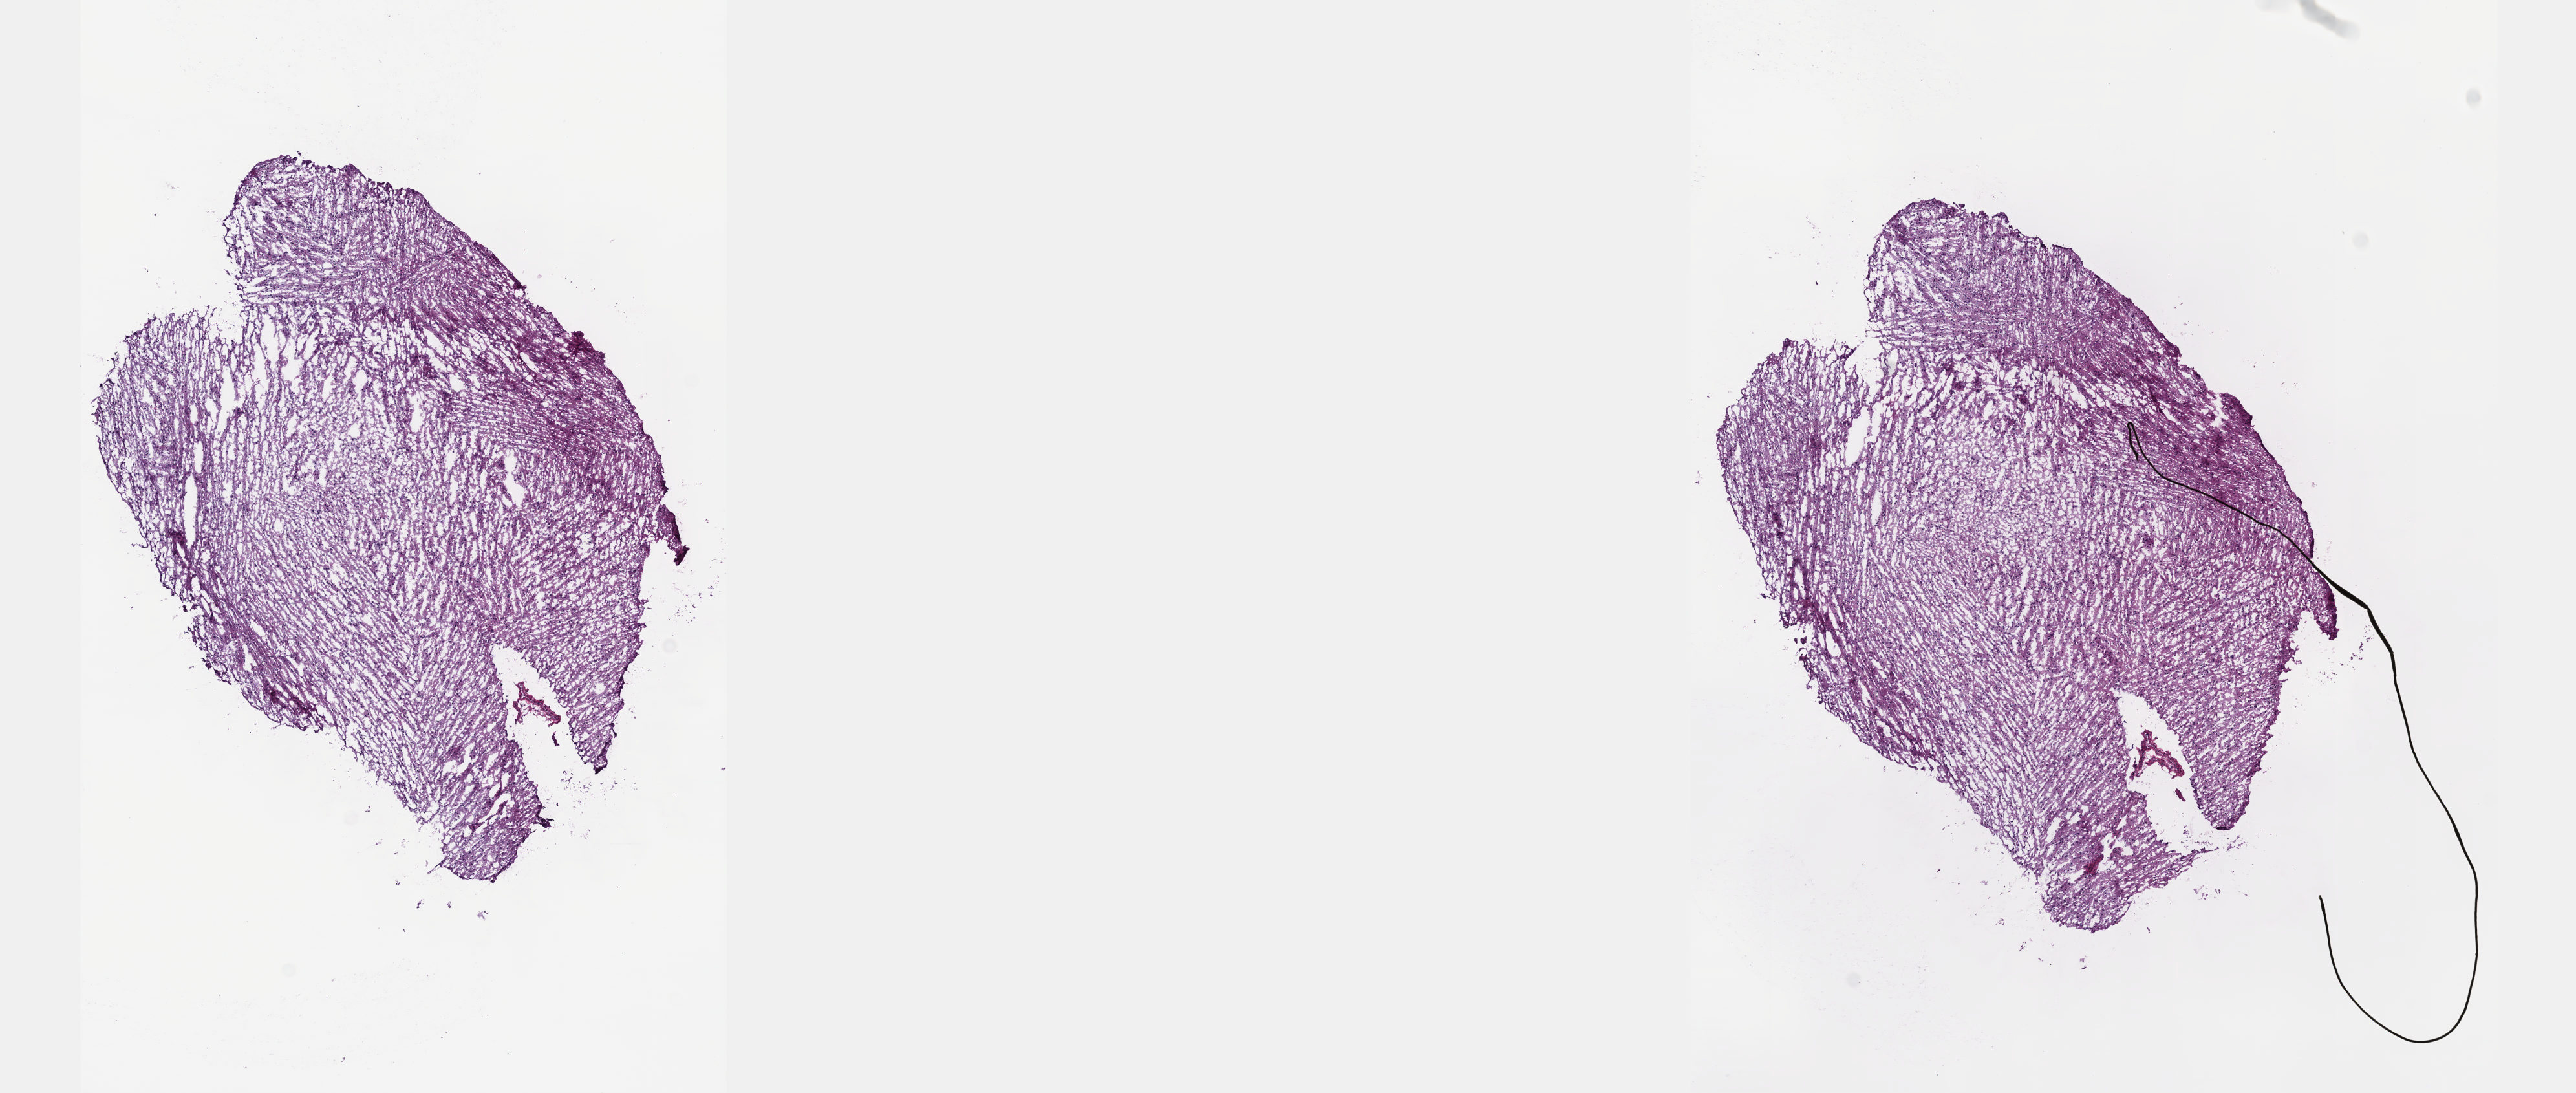
Digitized Hematoxylin and eosin (H&E) stained tissue section (whole slide) — a low-resolution overview of the entire scanned area, about 16.1 x 6.8 mm. Frozen section. Sample: primary tumour, brain. Male patient; age at initial diagnosis 19 years. Histologic grade: G2 (moderately differentiated). Composition of this section per pathologist review: tumour cells 45%, tumour nuclei 90%, normal cells 10%, stromal cells 45%, necrosis 0%. Infiltration values recorded for this section: lymphocyte infiltration 0%, monocyte infiltration 0%, neutrophil infiltration 0%.
• laterality: left
• histologic diagnosis: Mixed glioma (cerebrum)